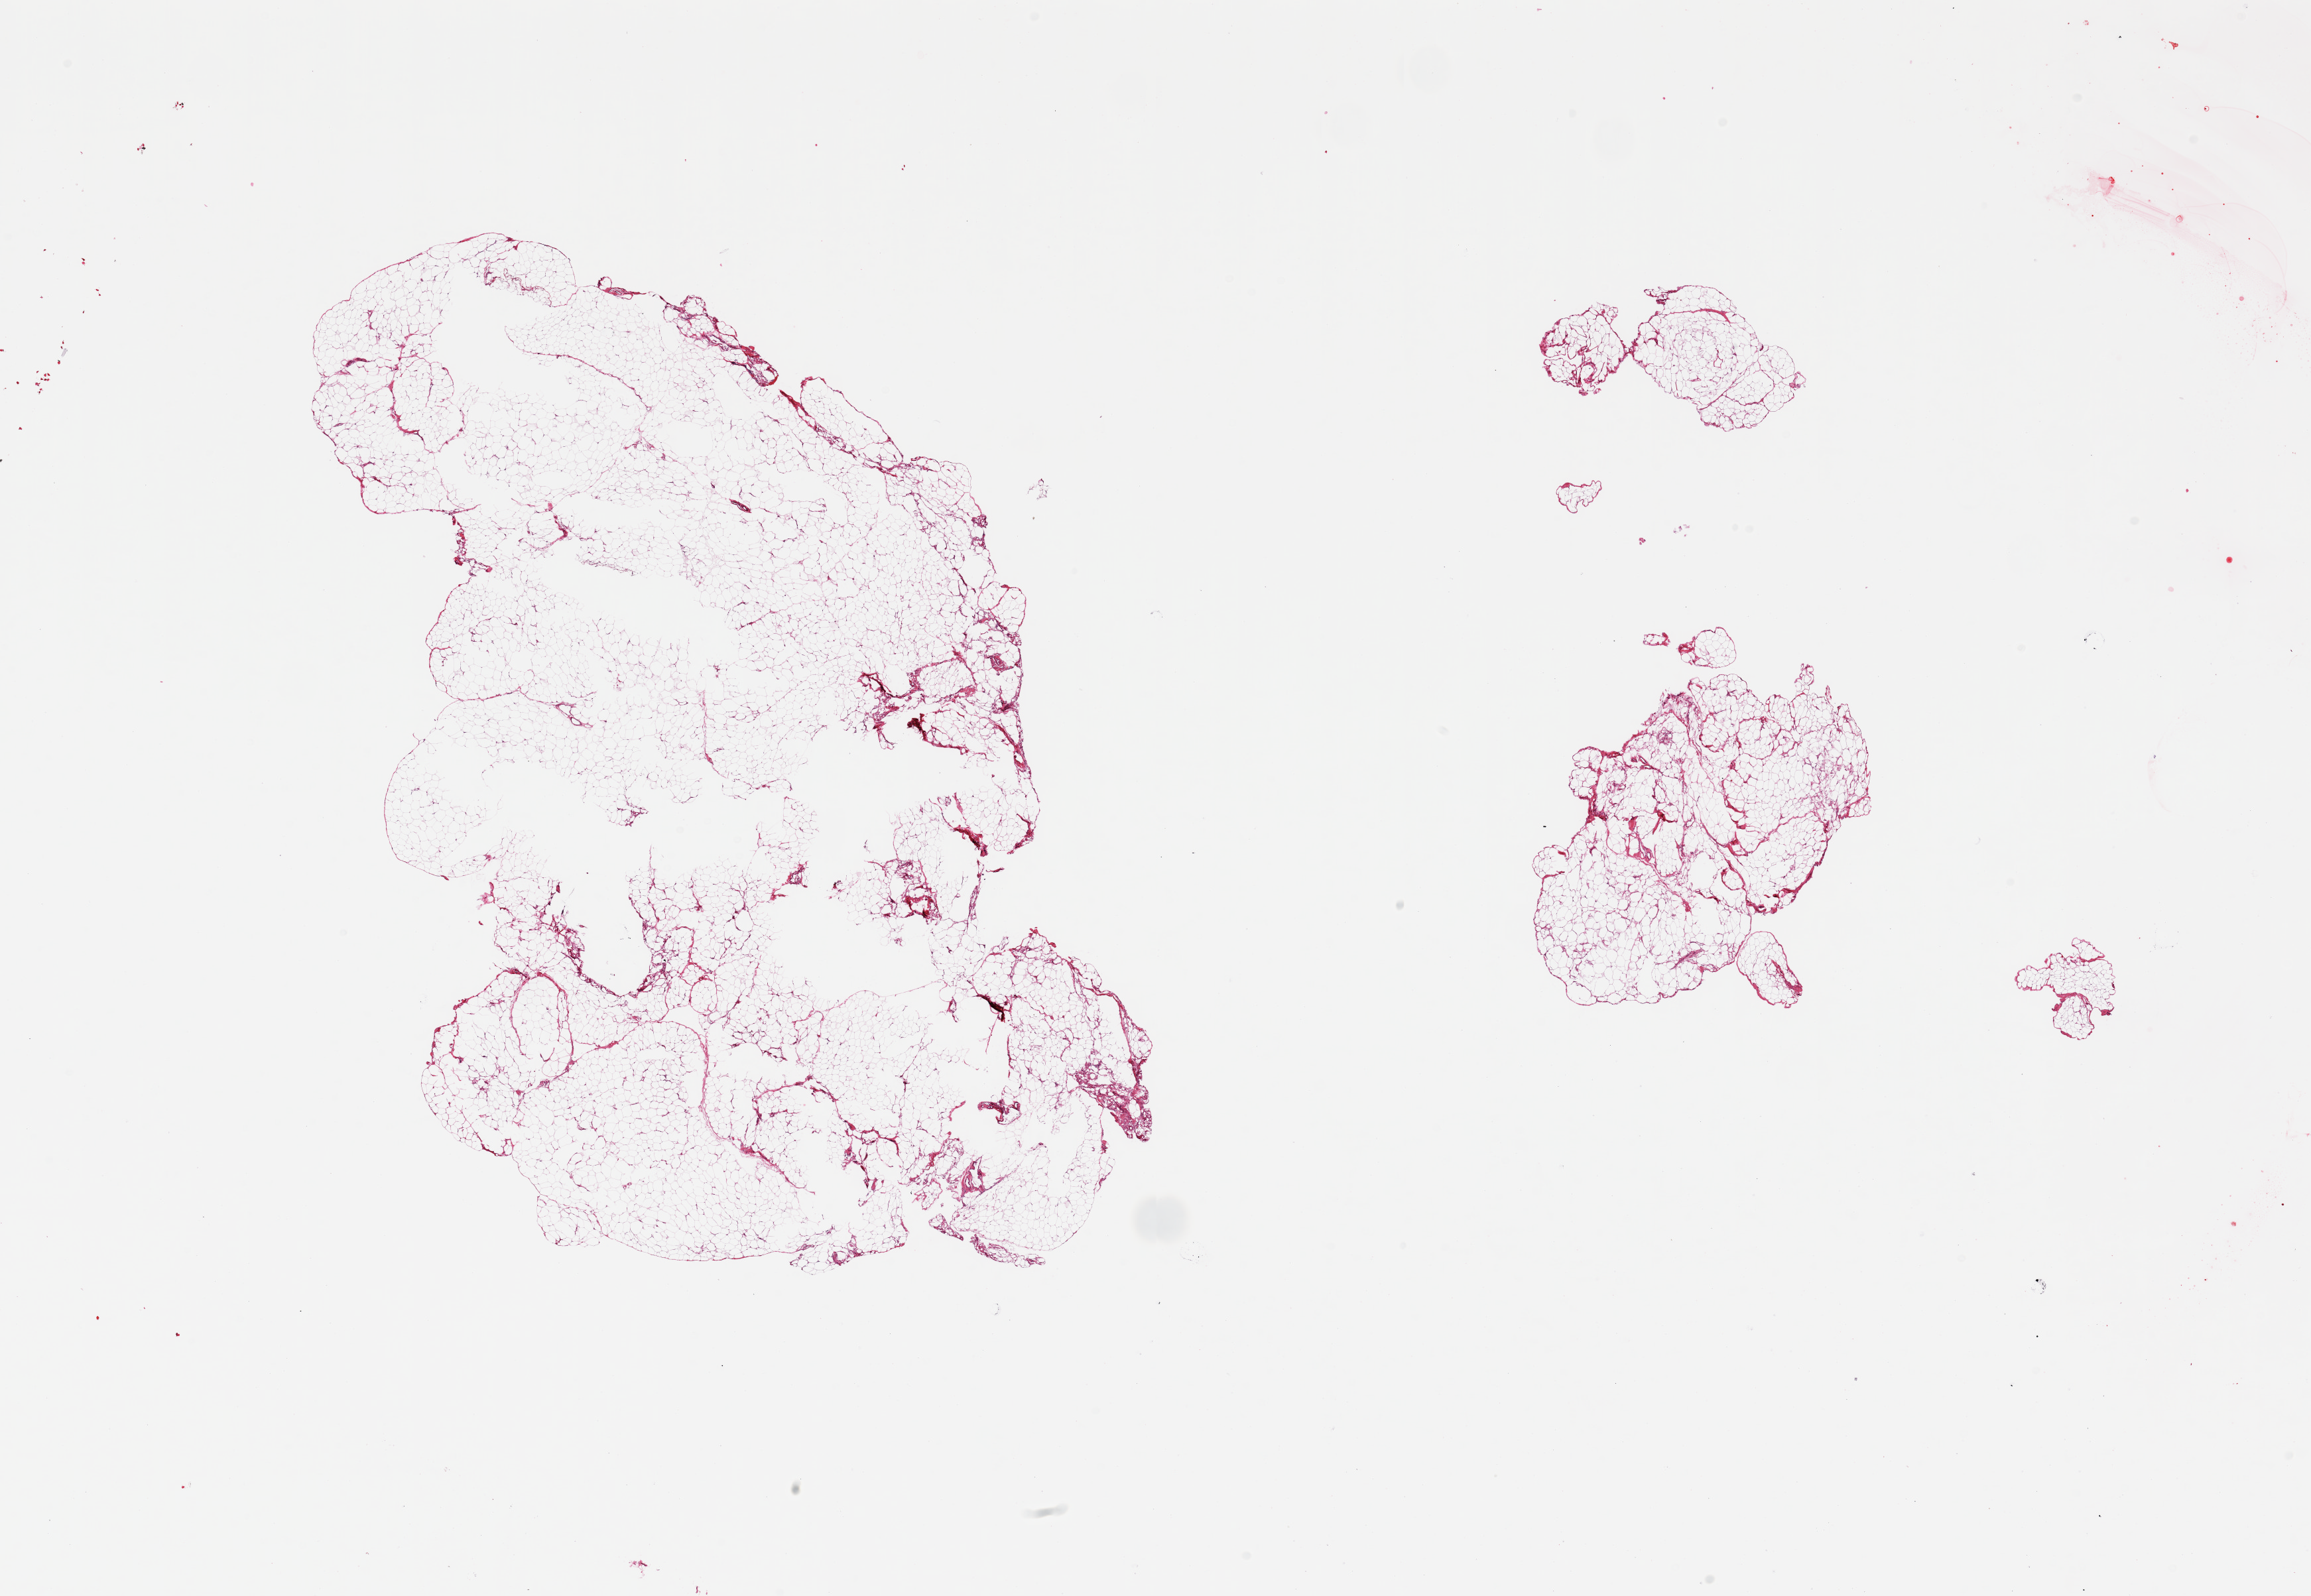
Whole-slide image, H&E stain, low-resolution overview of the scanned area, about 27.6 x 19.0 mm (acquisition: 20x scan). PAXgene-fixed paraffin-embedded (PFPE) section. Sampled site (target tissue): omentum. Tissue donor sample. Donor sex: male.
• review note (as recorded): 2 pieces; lobulated mature adipose tissue with fibrovascular component